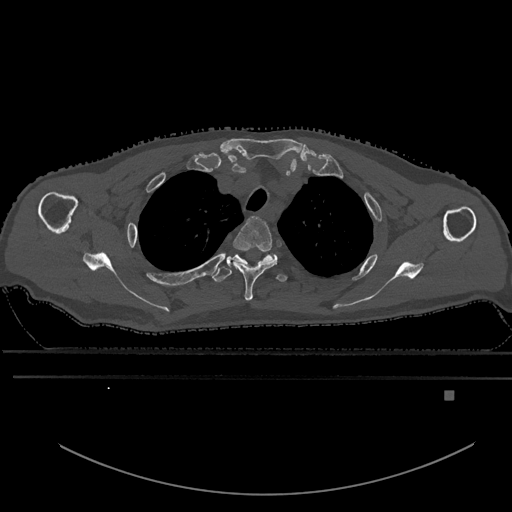
CT including the spine, one axial slice; position 481 of 969 along the scan axis; bone window (W 1800 / L 400 HU); 0.5 mm slice thickness; 512 × 512 image matrix, field of view 456 × 456 mm. Male patient, age 82 years. Case-level facts recorded for this patient, not image findings: primary cancer: prostate; vertebrae with lytic lesions (as recorded): T11, T9, T8, T2.
Structures marked on this image (semi-automatically segmented with operator editing):
- T2 vertebra: bounding box [x1, y1, x2, y2] px = [227, 217, 278, 301]
- T3 vertebra: [212, 254, 287, 283]